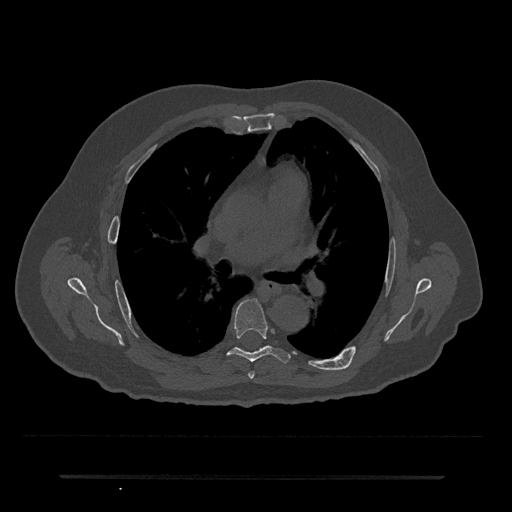
CT including the spine, one axial slice; position 437 of 797 along the scan axis; reconstruction kernel Br40s/3; 120 kVp; bone window (W 1800 / L 400 HU); 0.5 mm slice thickness; 512 × 512 image matrix, field of view 437 × 437 mm. Patient: male, 69 years. Case-level facts recorded for this patient, not image findings: primary cancer: prostate.
Outlined on this slice (semi-automatic segmentation, software-assisted and operator-edited):
- T5 vertebra: bounding box (x1, y1, x2, y2) in pixels: (248, 371, 255, 379)
- T6 vertebra: (228, 298, 290, 363)